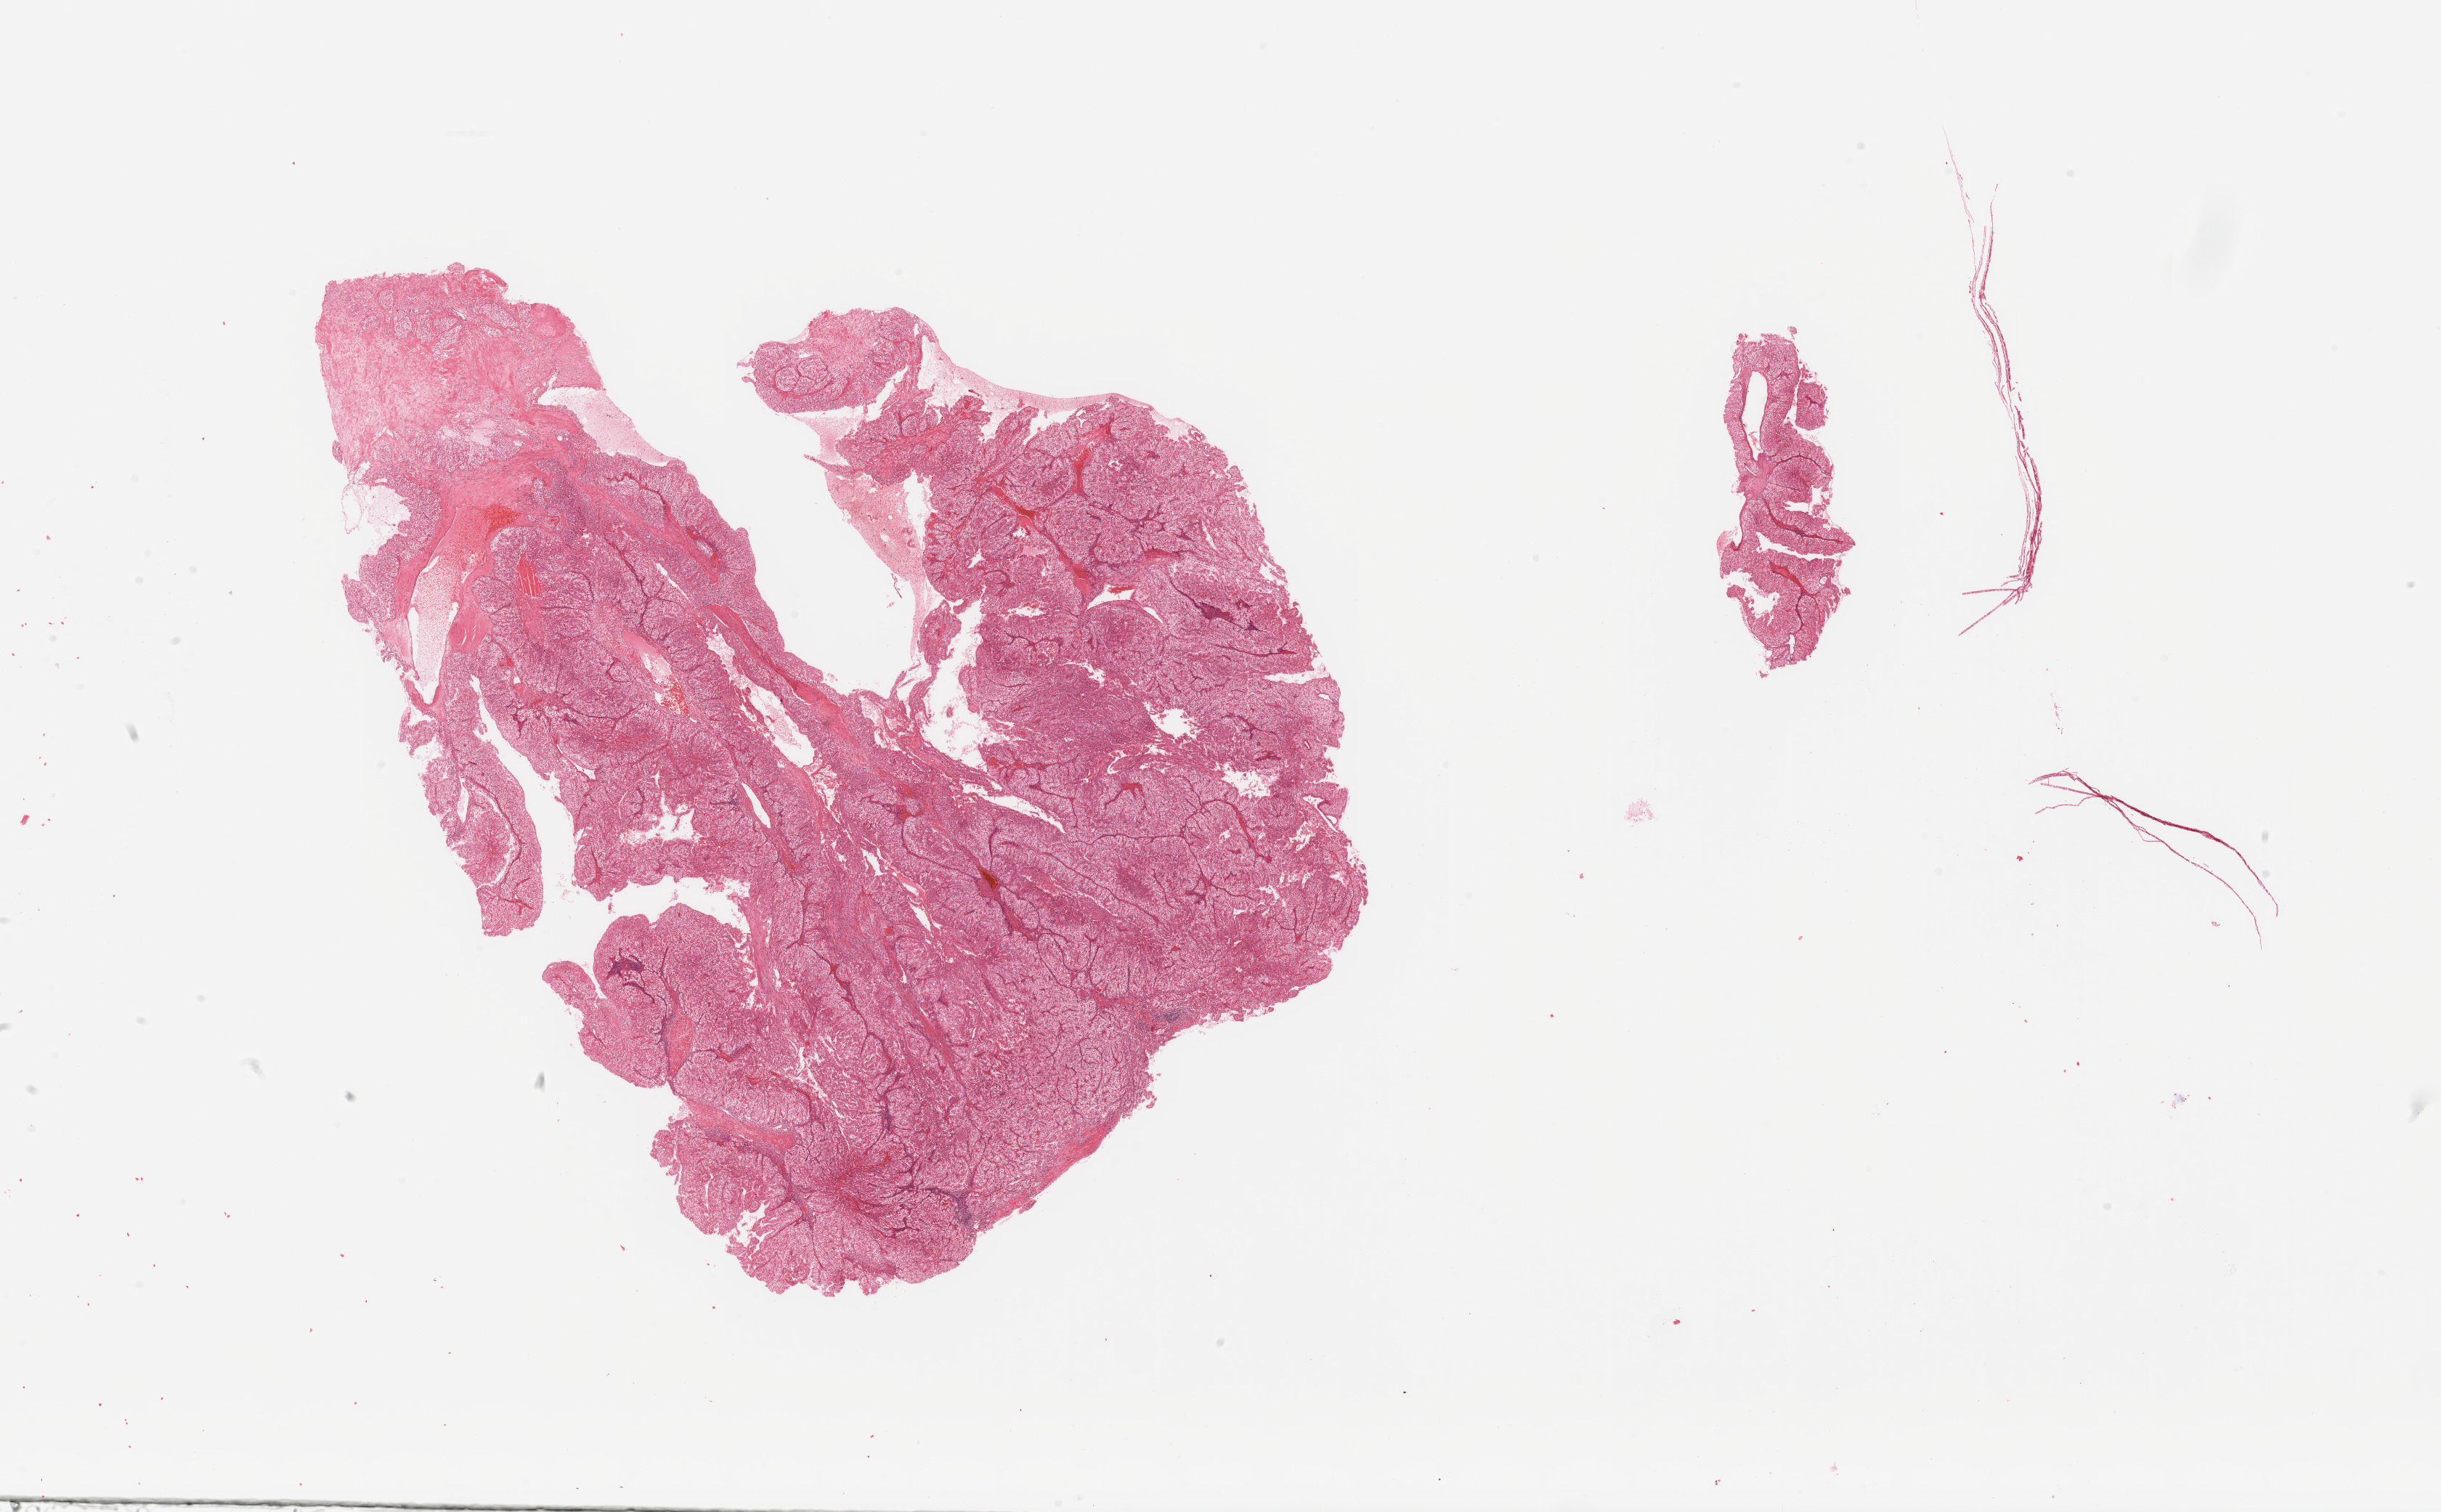
H&E-stained whole-slide image, shown as a low-resolution overview of the whole scanned area (about 26.6 x 16.5 mm, from a 20x scan). Tumour tissue sample, sampled site: kidney. Patient: male, age 61 years. Histologic grade: G2 (moderately differentiated). Pathologist review of this section (percent, as recorded): tumour nuclei 95%, necrosis 5%.
• AJCC pathologic stage: II
• diagnosis: Renal cell carcinoma, NOS